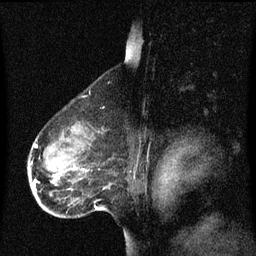
Breast MRI (dynamic contrast-enhanced), one sagittal slice. Slice 46 of 60 in the series (ordered by position). Dynamic contrast-enhanced series, image 2 of 3 at this slice position (ordered by acquisition). 1.5 T. TE 4.2 ms, TR 8.4 ms. 256 × 256 image matrix. Patient: female, 49 years. From the clinical record (not read from this slice): setting: breast cancer imaged before/during neoadjuvant chemotherapy; receptor status: HR-positive, HER2-negative.
Annotated regions visible in this slice (semi-automatic segmentation, software-assisted and operator-edited):
- analysis volume of interest (the breast-tissue region the enhancement analysis was run in; not a lesion): bounding box [x1, y1, x2, y2] px = [29, 126, 112, 201]
- tumour enhancement mask (voxels above the 70 % enhancement threshold inside the analysis volume of interest): [34, 144, 39, 187]